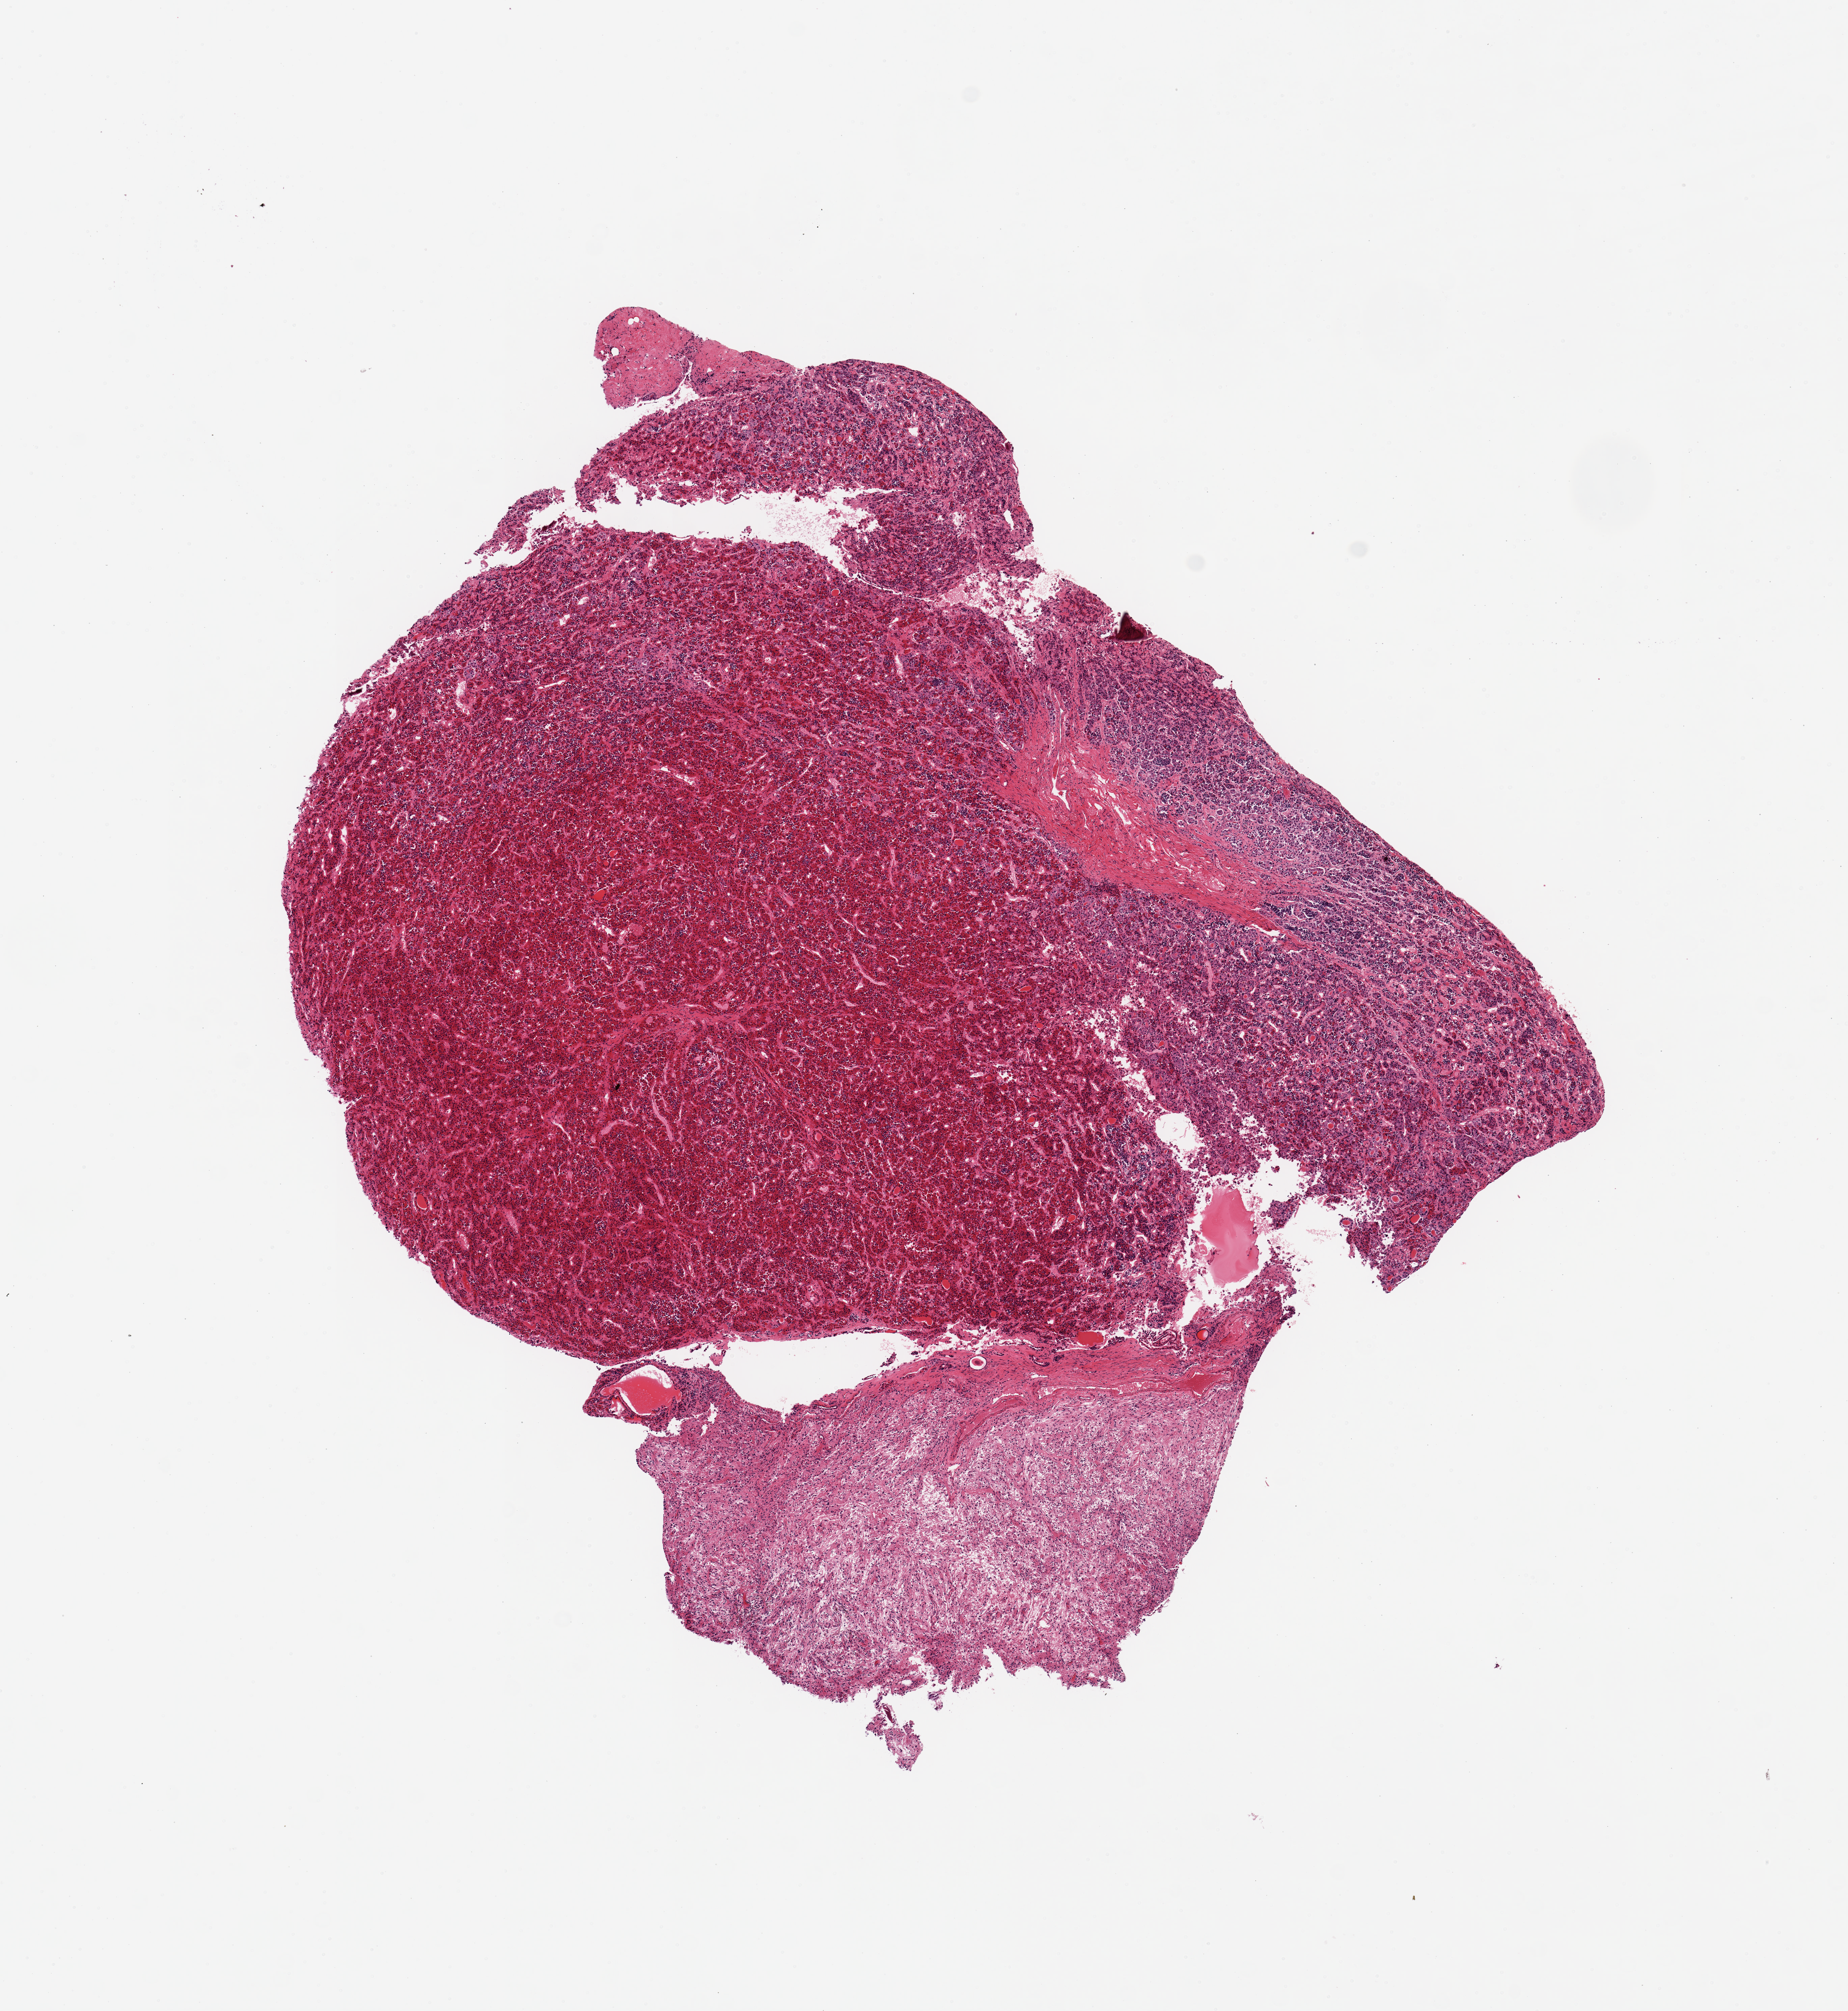
Digitized H&E-stained section, brightfield — whole scanned area (about 10.8 x 11.8 mm) shown as a low-resolution overview; PAXgene-fixed paraffin-embedded (PFPE) section; sampled site (target tissue): pituitary; tissue donor sample.
Reviewer comment on this tissue sample: 1 piece; ~80% adenohypophysis, ~20% neurohypophysis.